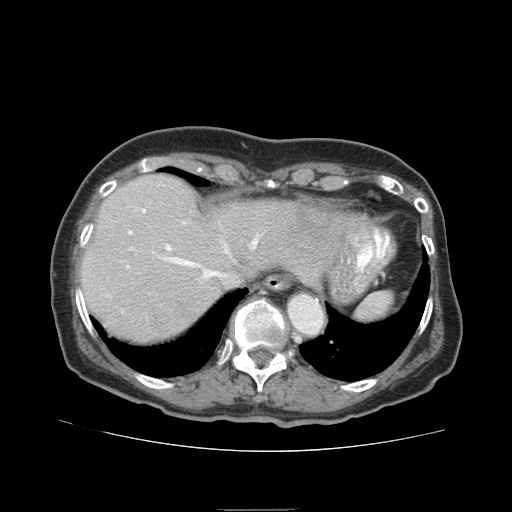
Contrast-enhanced abdominal CT (liver protocol), one axial slice. 140 kVp. Soft-tissue window (W 400 / L 40 HU). 2.5 mm slice thickness. 512 × 512 image matrix, field of view 360 × 360 mm. Case-level facts recorded for this patient, not image findings: diagnosis: hepatocellular carcinoma (patient treated with transarterial chemoembolisation; whether this scan precedes or follows treatment is not stated here); TNM stage (as recorded): Stage-IVA; Child-Pugh class: B.
Structures marked on this image (semi-automatically segmented with operator editing):
- liver parenchyma outside the tumour (the mass and vessels are separate outlines, so this box may not span the whole liver): bounding box <80,174,363,342> (left, top, right, bottom; pixels)
- mass: <150,296,189,335>
- liver vessels: <126,209,258,278>